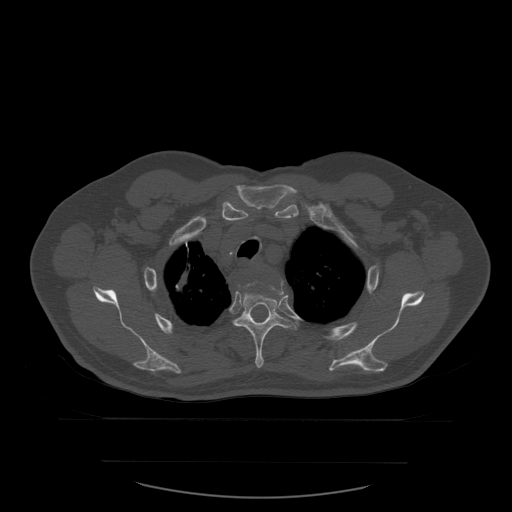
CT including the spine, one axial slice; bone window (W 1800 / L 400 HU); 1.25 mm slice thickness; 512 × 512 image matrix. Patient age 71 years. Case-level facts recorded for this patient, not image findings: primary cancer: lung.
Structures marked on this image (semi-automatically segmented with operator editing):
- T3 vertebra: bounding box [x1, y1, x2, y2] px = [242, 278, 284, 295]
- T4 vertebra: [233, 282, 297, 369]